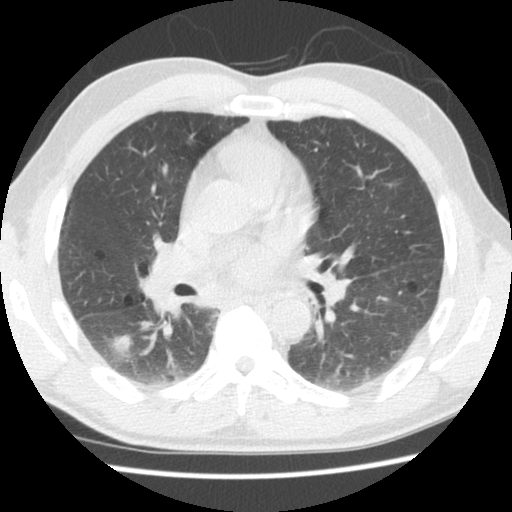
Low-dose screening chest CT, one axial slice; slice 80 of 133 in the series (ordered by position); lung window (W 1500 / L -600 HU); 2.5 mm slice thickness; 512 × 512 image matrix, field of view 320 × 320 mm.
Outlined on this slice (expert manual segmentation):
- lesion 1 (tumor, lower lobe of right lung): box from (x=110, y=335) to (x=134, y=356) px